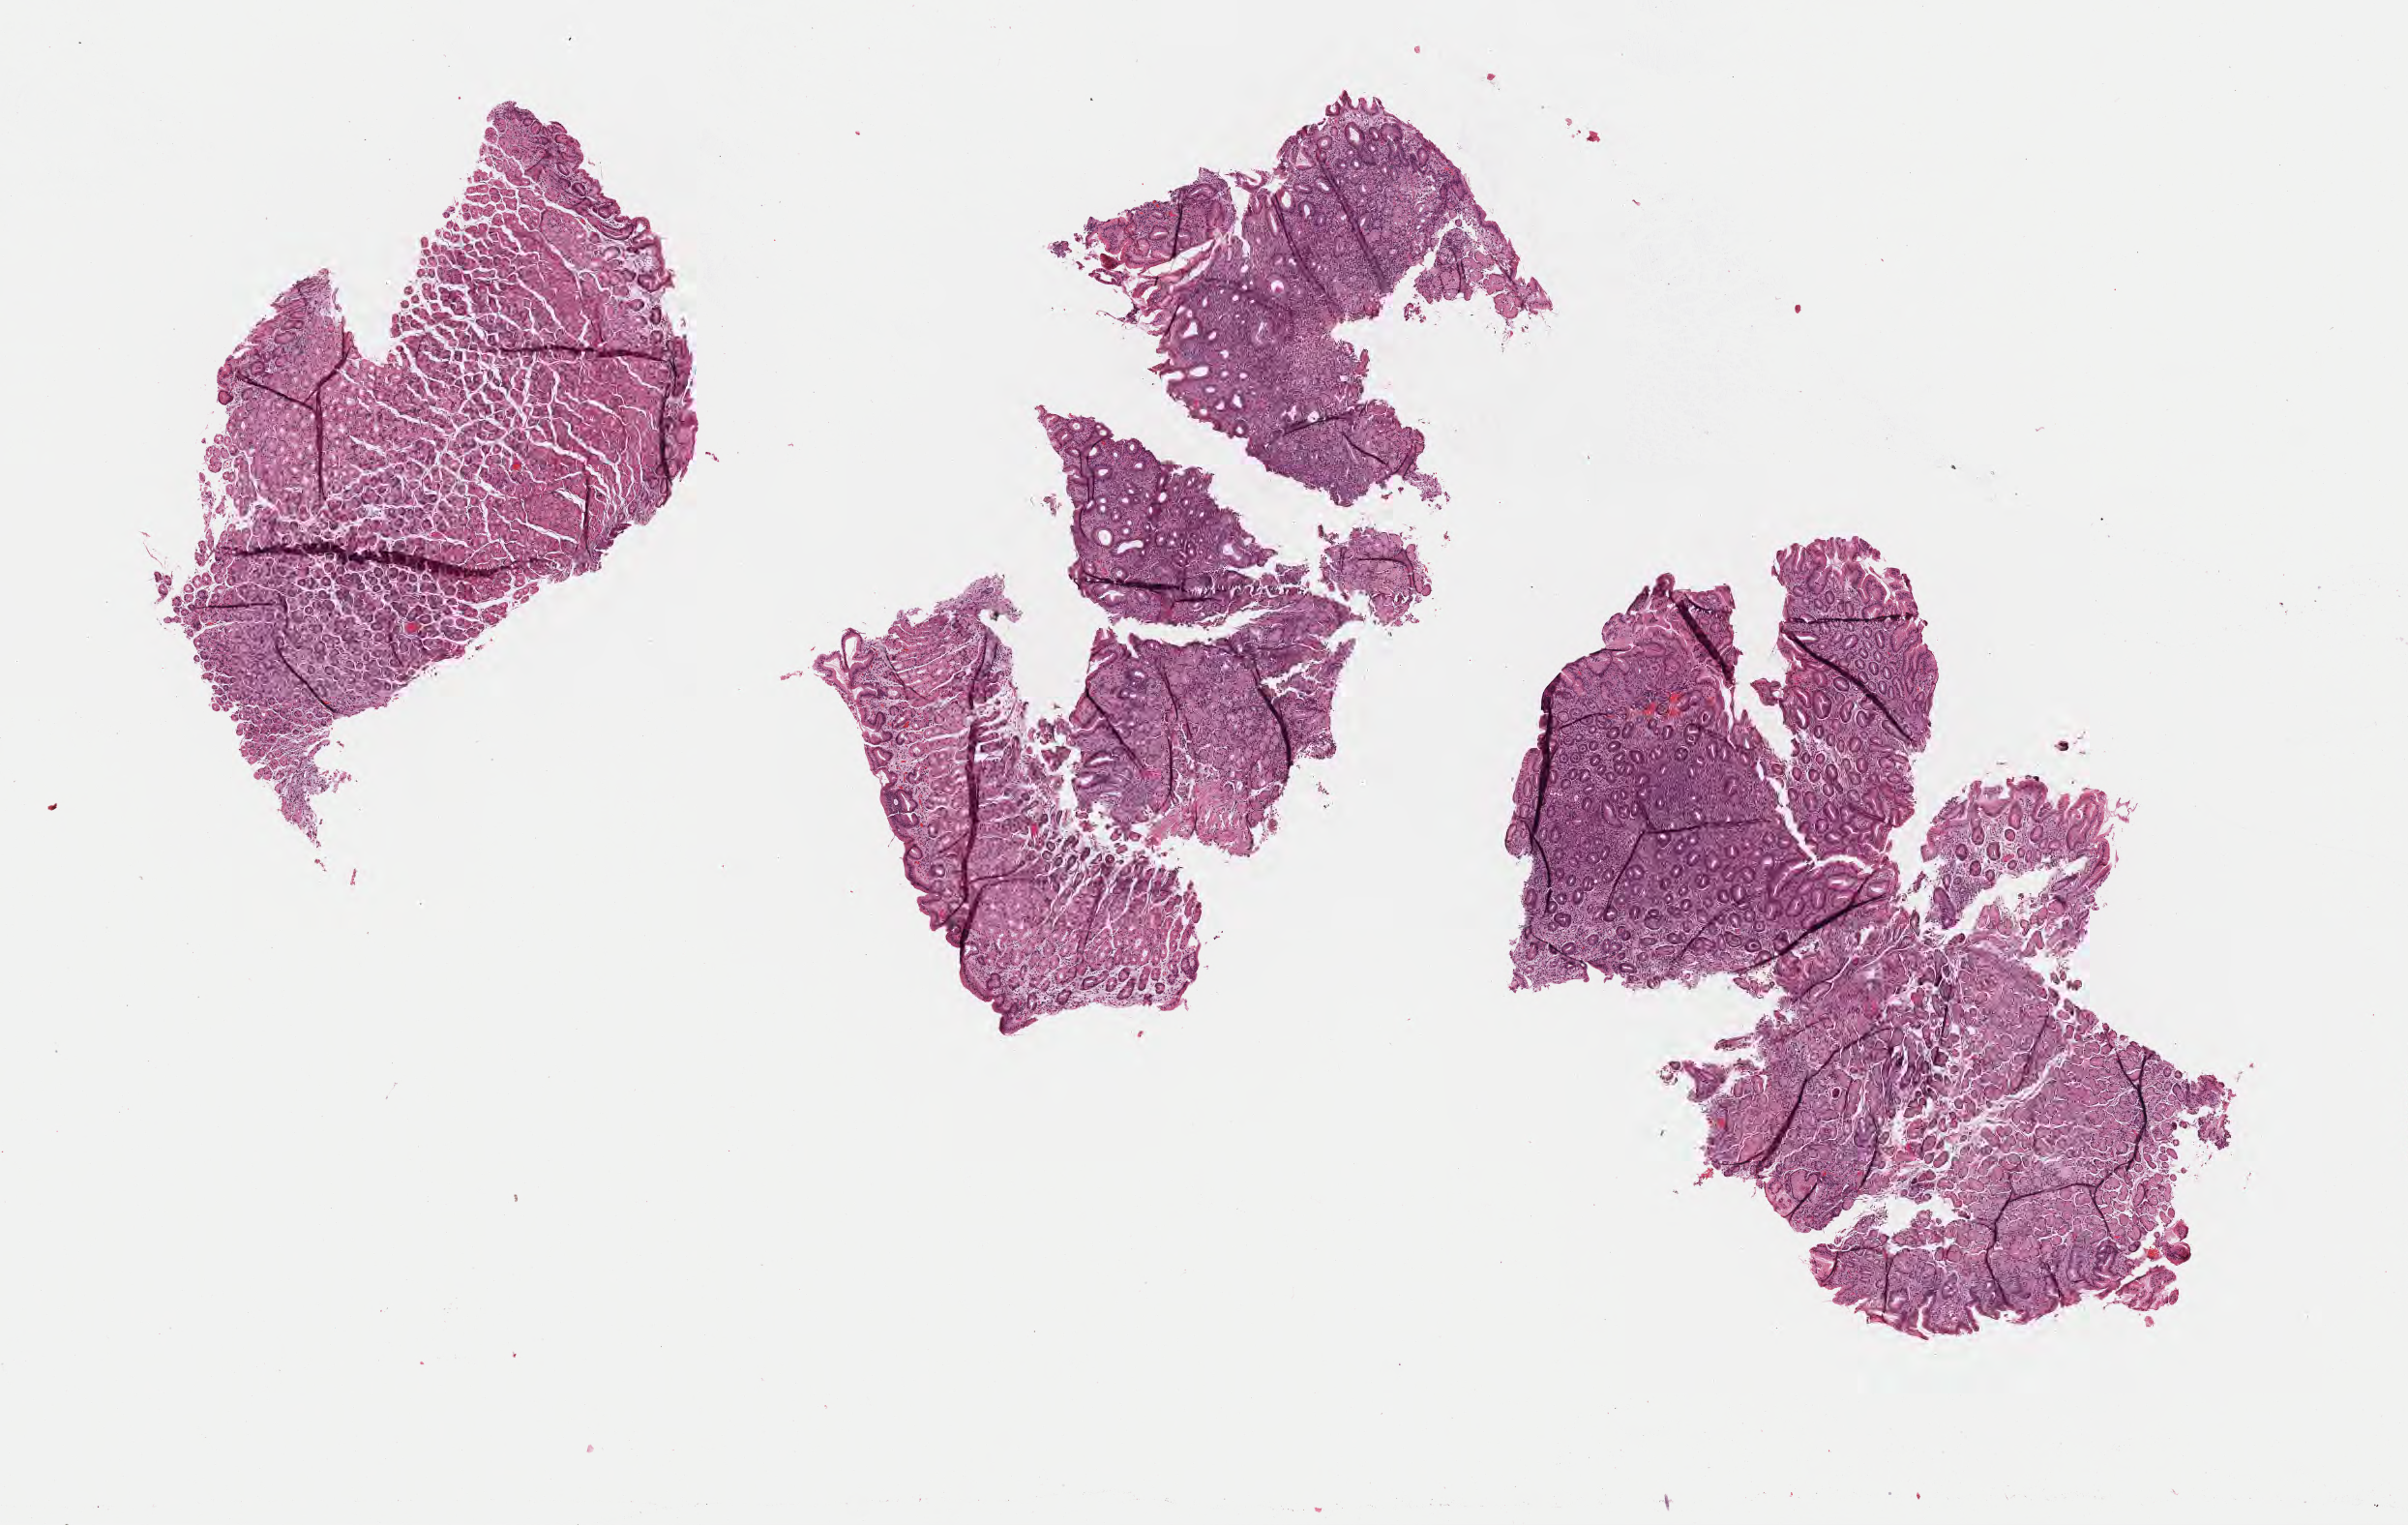
Haematoxylin and eosin whole-slide image — low-resolution overview of the scanned area, about 10.1 x 6.4 mm; formalin-fixed, paraffin-embedded (FFPE) tissue; non-tumor (normal tissue) sample from a patient with diffuse large B-cell lymphoma, NOS. Patient male; 60 years old. Slide review estimates, as recorded: tumor cells 0%, tumor nuclei 0%, stromal cells 30%, necrosis 0%, normal cells 70%. Inflammatory infiltration, as recorded: lymphocyte infiltration 40%, monocyte infiltration 20%, neutrophil infiltration 10%.
This section: non-tumor tissue sample; the patient's diagnosis is given above.